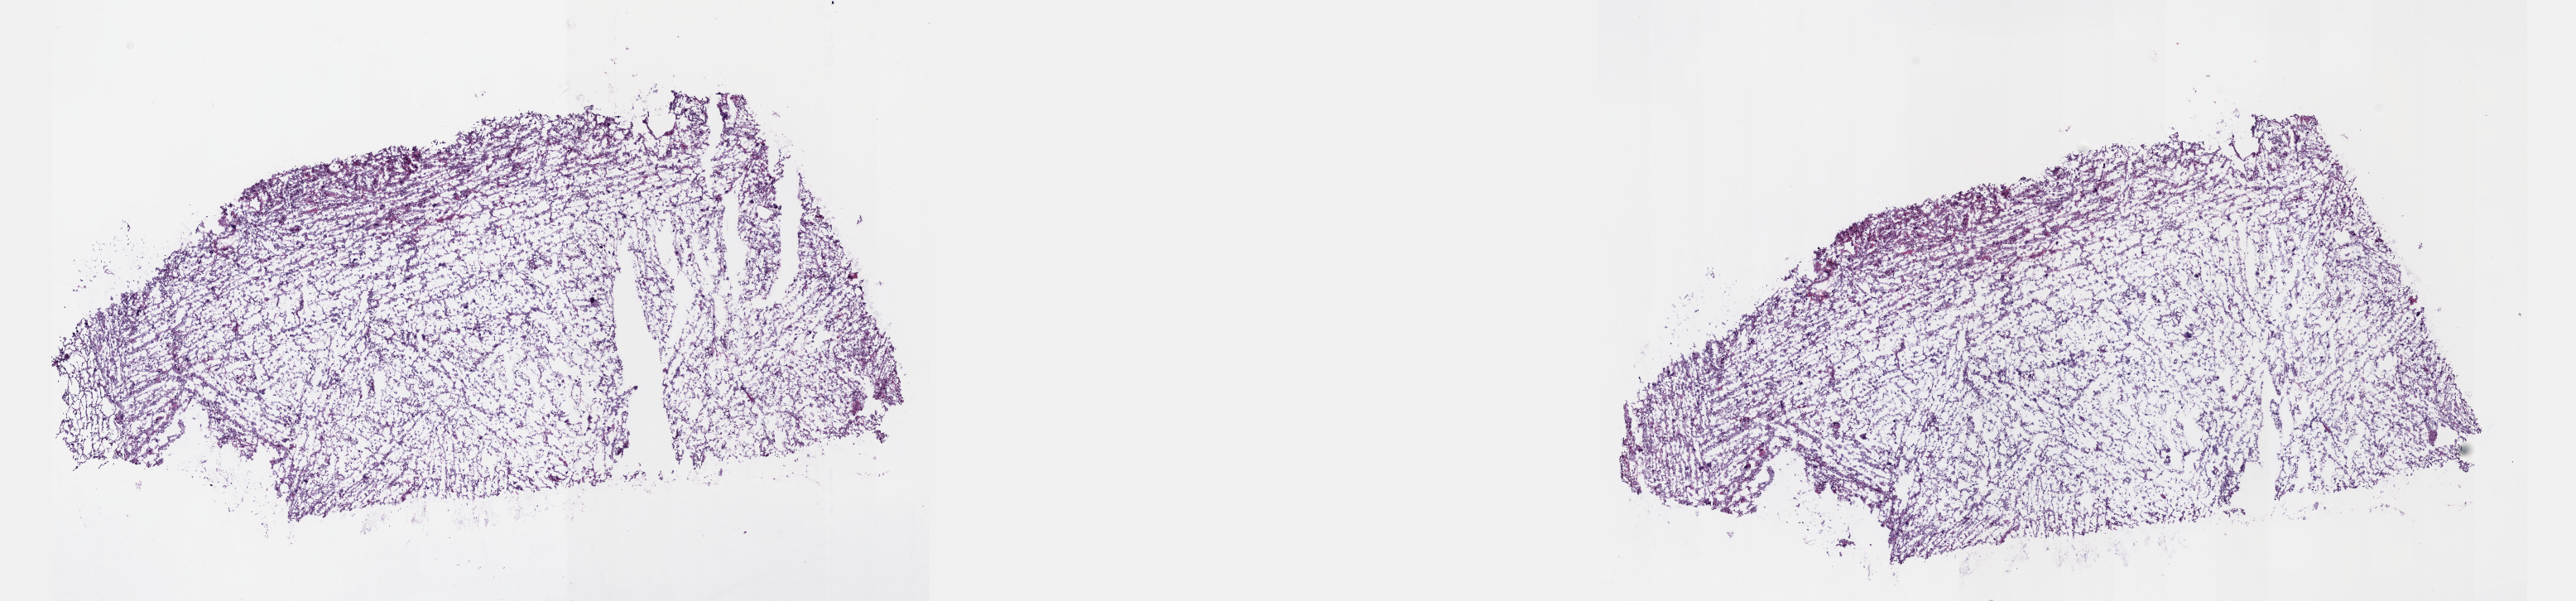
Whole-slide histology image, H&E, shown as a low-resolution overview of the whole scanned area (about 25.1 x 5.9 mm, acquisition: 40x scan), frozen section, connective, subcutaneous and other soft tissues, primary tumour sample. Female, age 54 years at initial diagnosis. Composition of this section per pathologist review: tumour cells 100%, tumour nuclei 75%.
Diagnosis: Fibromyxosarcoma (connective, subcutaneous and other soft tissues of lower limb and hip).